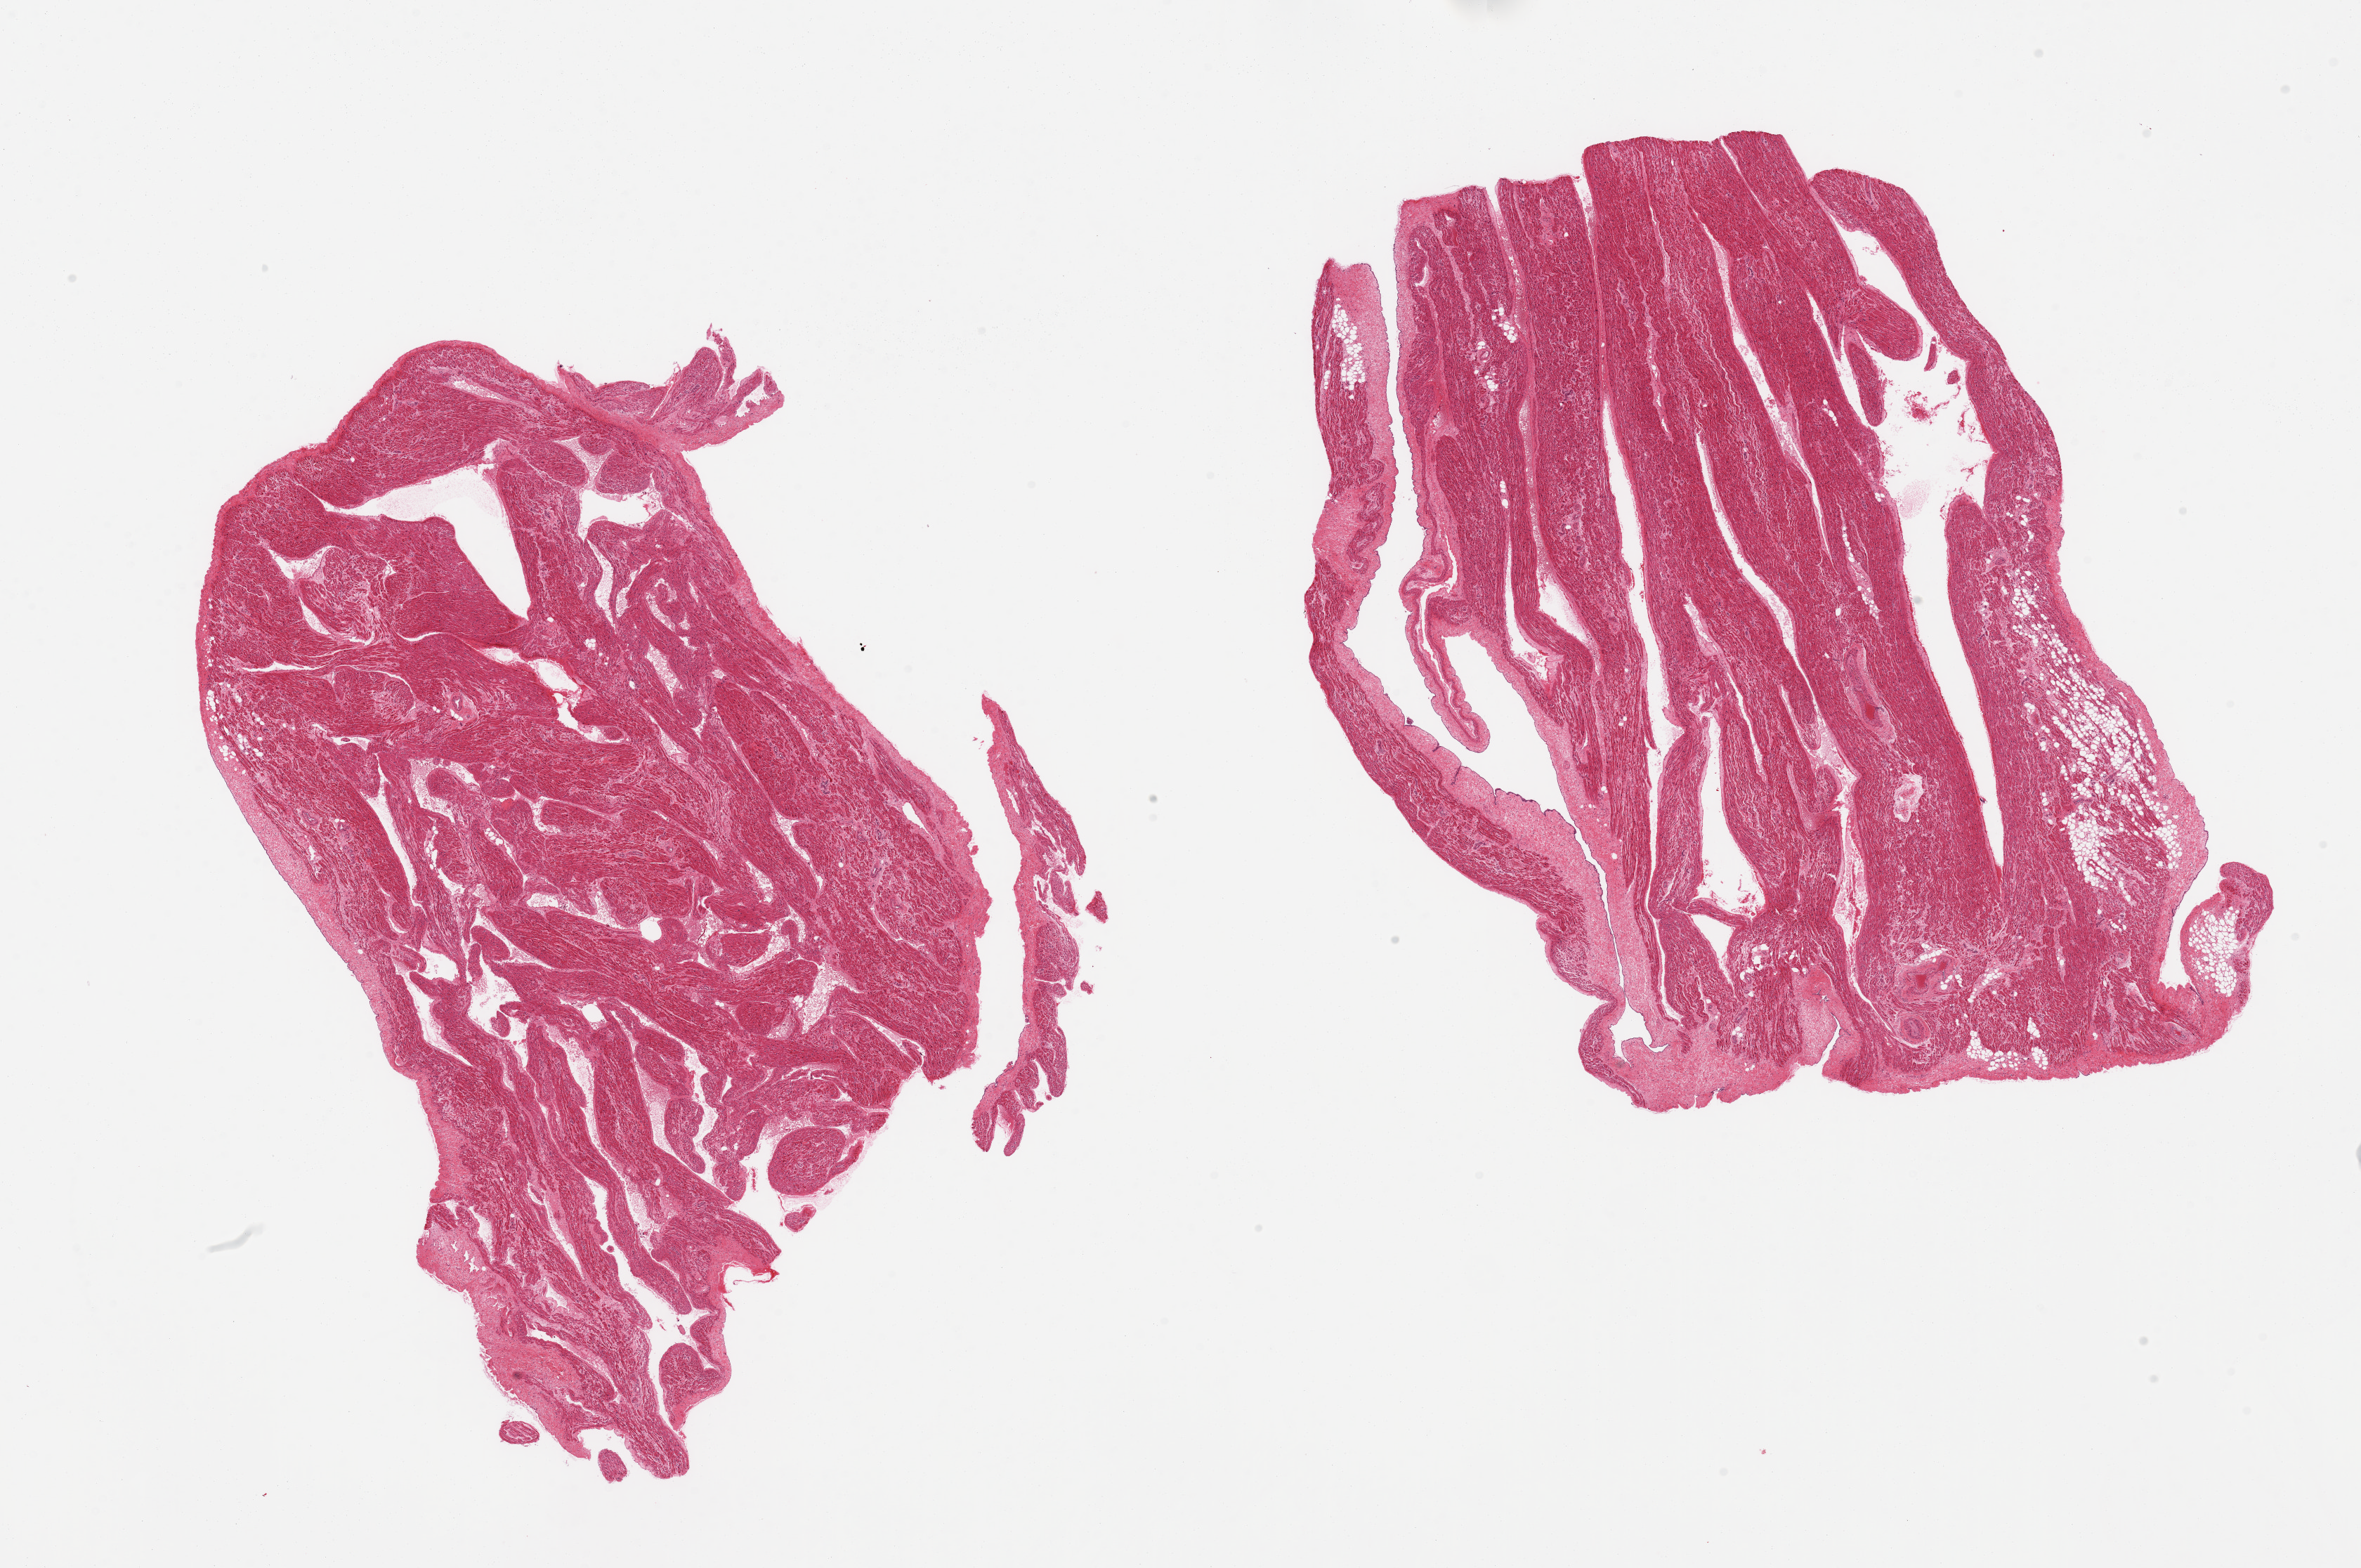
H&E whole-slide image, a low-resolution overview of the entire scanned area, about 26.6 x 17.7 mm (from a 20x scan). PAXgene-fixed paraffin-embedded (PFPE) section. Section of auricular appendage (target tissue). Donor tissue sample.
Pathologist's review note for this sample: 2 pieces, <10% fat.